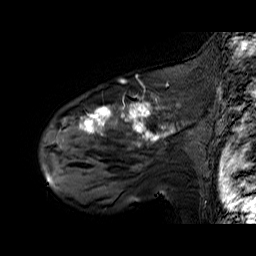
Breast MRI (dynamic contrast-enhanced), one sagittal slice. Position 46 of 60 along the scan axis. Dynamic contrast-enhanced series, time point 2 of 6 at this slice position (early post-contrast). 1.5 T. TE 6.3 ms, TR 32.9 ms. 4 mm slice thickness. 256 × 256 image matrix. Female patient. From the clinical record (not read from this slice): setting: breast cancer imaged before/during neoadjuvant chemotherapy; receptor status: HER2-positive.
Structures marked on this image (semi-automatically segmented with operator editing):
- analysis volume of interest (the breast-tissue region the enhancement analysis was run in; not a lesion): bounding box (x1, y1, x2, y2) in pixels: (48, 92, 195, 174)
- tumour enhancement mask (voxels above the 100 % enhancement threshold inside the analysis volume of interest): (79, 102, 175, 146)